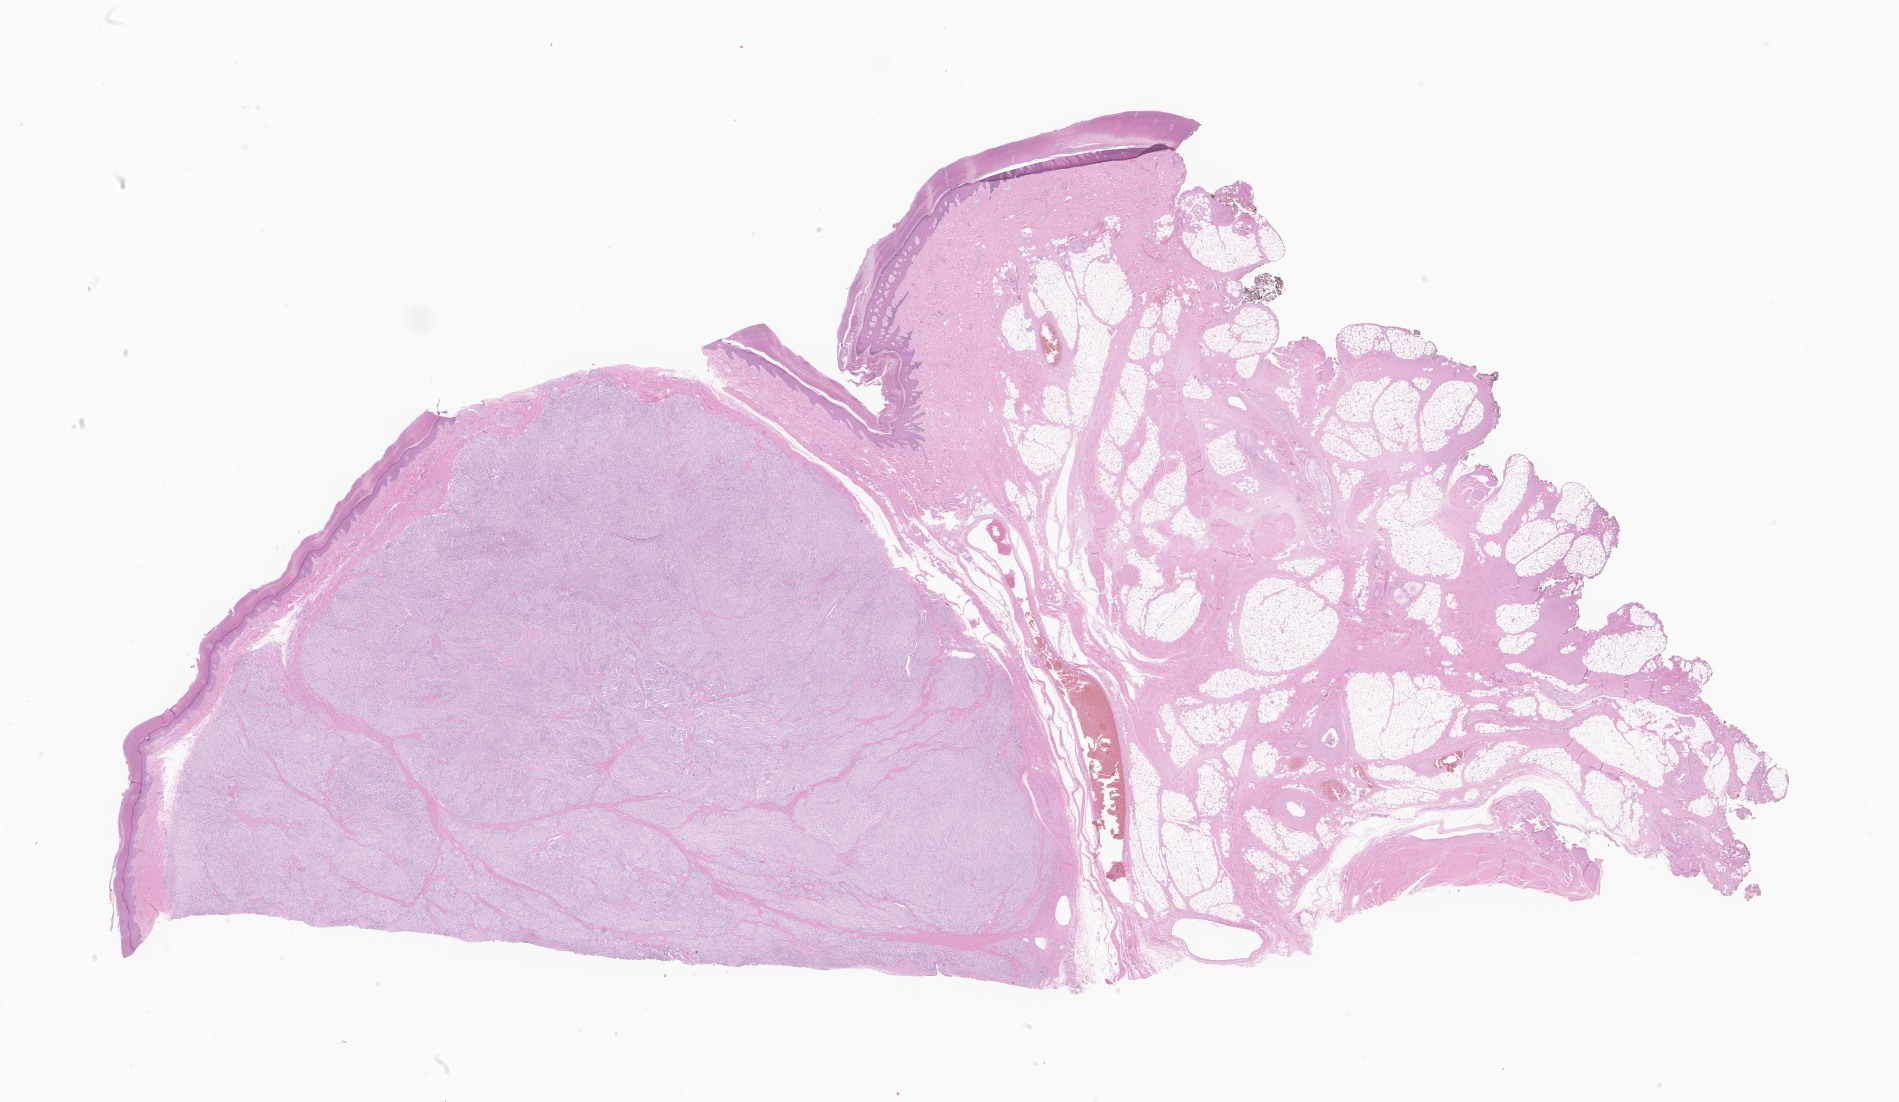
Digitized hematoxylin and eosin (H&E)-stained section of tumor tissue from the soft tissue, shown as a low-resolution overview of the whole scanned area (about 32.0 x 18.6 mm), formalin-fixed, paraffin-embedded (FFPE) tissue. Patient female; age 236 months (19 years 8 months).
* diagnosis (ICD-O-3 morphology term): Clear cell sarcoma, NOS